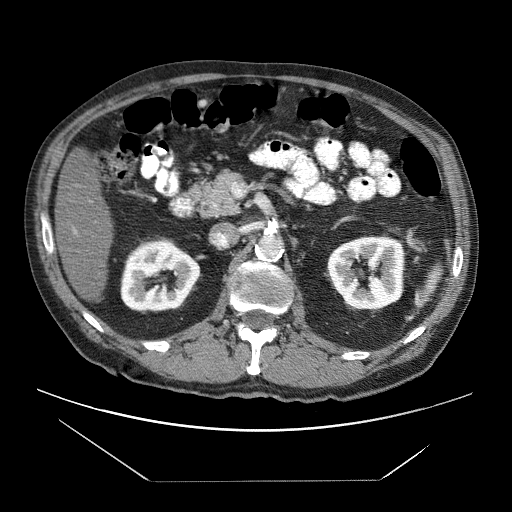
Contrast-enhanced abdominal CT (liver protocol), one axial slice; 120 kVp; soft-tissue window (W 400 / L 40 HU); 2.5 mm slice thickness; 512 × 512 image matrix. Case-level facts recorded for this patient, not image findings: diagnosis: hepatocellular carcinoma (patient treated with transarterial chemoembolisation; whether this scan precedes or follows treatment is not stated here); TNM stage (as recorded): Stage-IVB; Child-Pugh class: B; tumour differentiation: poorly differentiated; tumour nodularity: uninodular.
Outlined on this slice (semi-automatic segmentation, software-assisted and operator-edited):
- liver parenchyma outside the tumour (the mass and vessels are separate outlines, so this box may not span the whole liver): bounding box [x1, y1, x2, y2] px = [54, 150, 112, 302]
- liver vessels: [74, 231, 76, 233]